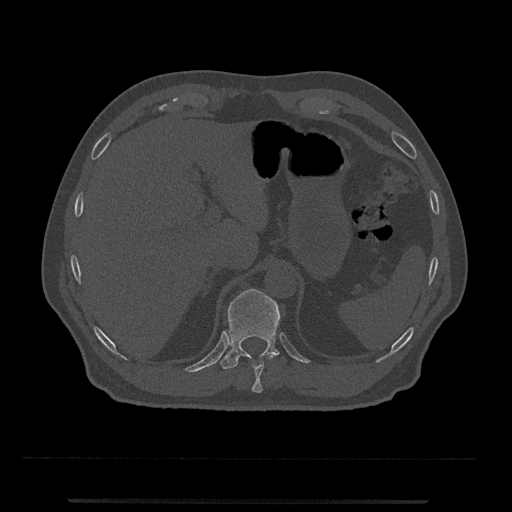
CT including the spine, one axial slice; position 483 of 797 along the scan axis; reconstruction kernel Br40s/3; bone window (W 1800 / L 400 HU); 0.5 mm slice thickness; 512 × 512 image matrix. Male patient, age 63 years. Case-level facts recorded for this patient, not image findings: primary cancer: prostate.
Outlined on this slice (semi-automatic segmentation, software-assisted and operator-edited):
- T10 vertebra: box from (x=252, y=354) to (x=275, y=393) px
- T11 vertebra: (x=220, y=288)–(x=280, y=369)